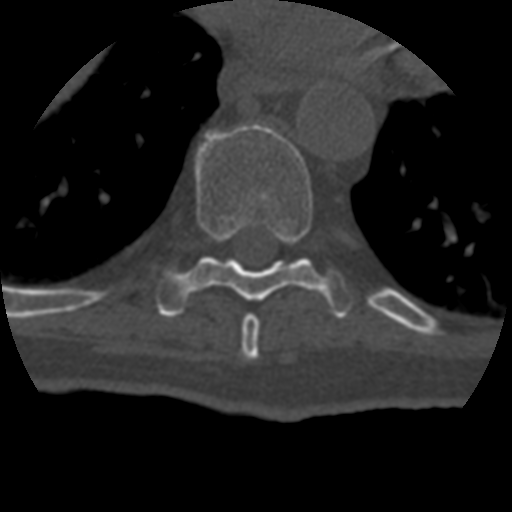
CT including the spine, one axial slice. Position 239 of 399 along the scan axis. 120 kVp. Bone window (W 1800 / L 400 HU). 512 × 512 image matrix, field of view 160 × 160 mm. Patient age 69 years. From the clinical record (not read from this slice): primary cancer: prostate.
Outlined on this slice (semi-automatically segmented with operator editing):
- T8 vertebra: bounding box <242,314,260,360> (left, top, right, bottom; pixels)
- T9 vertebra: <158,124,353,318>